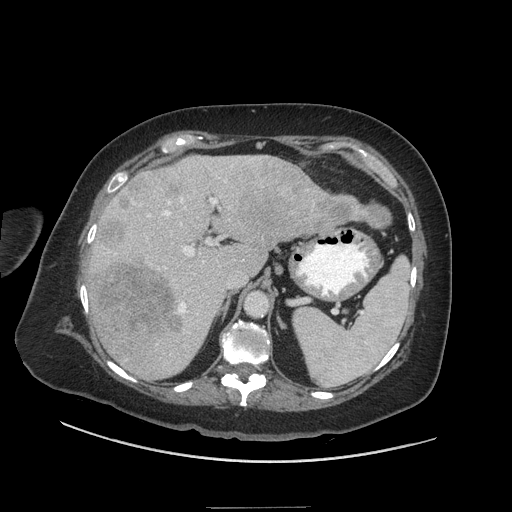
Contrast-enhanced abdominal CT (liver protocol), one axial slice; position 33 of 81 along the scan axis; reconstruction kernel STANDARD; soft-tissue window (W 400 / L 40 HU); 2.5 mm slice thickness; 512 × 512 image matrix. From the clinical record (not read from this slice): diagnosis: hepatocellular carcinoma (patient treated with transarterial chemoembolisation; whether this scan precedes or follows treatment is not stated here); TNM stage (as recorded): Stage-II; Child-Pugh class: A; tumour nodularity: multinodular.
Structures marked on this image (semi-automatically segmented with operator editing):
- liver parenchyma outside the tumour (the mass and vessels are separate outlines, so this box may not span the whole liver): bounding box <90,154,348,379> (left, top, right, bottom; pixels)
- mass: <89,162,392,341>
- liver vessels: <101,157,261,356>